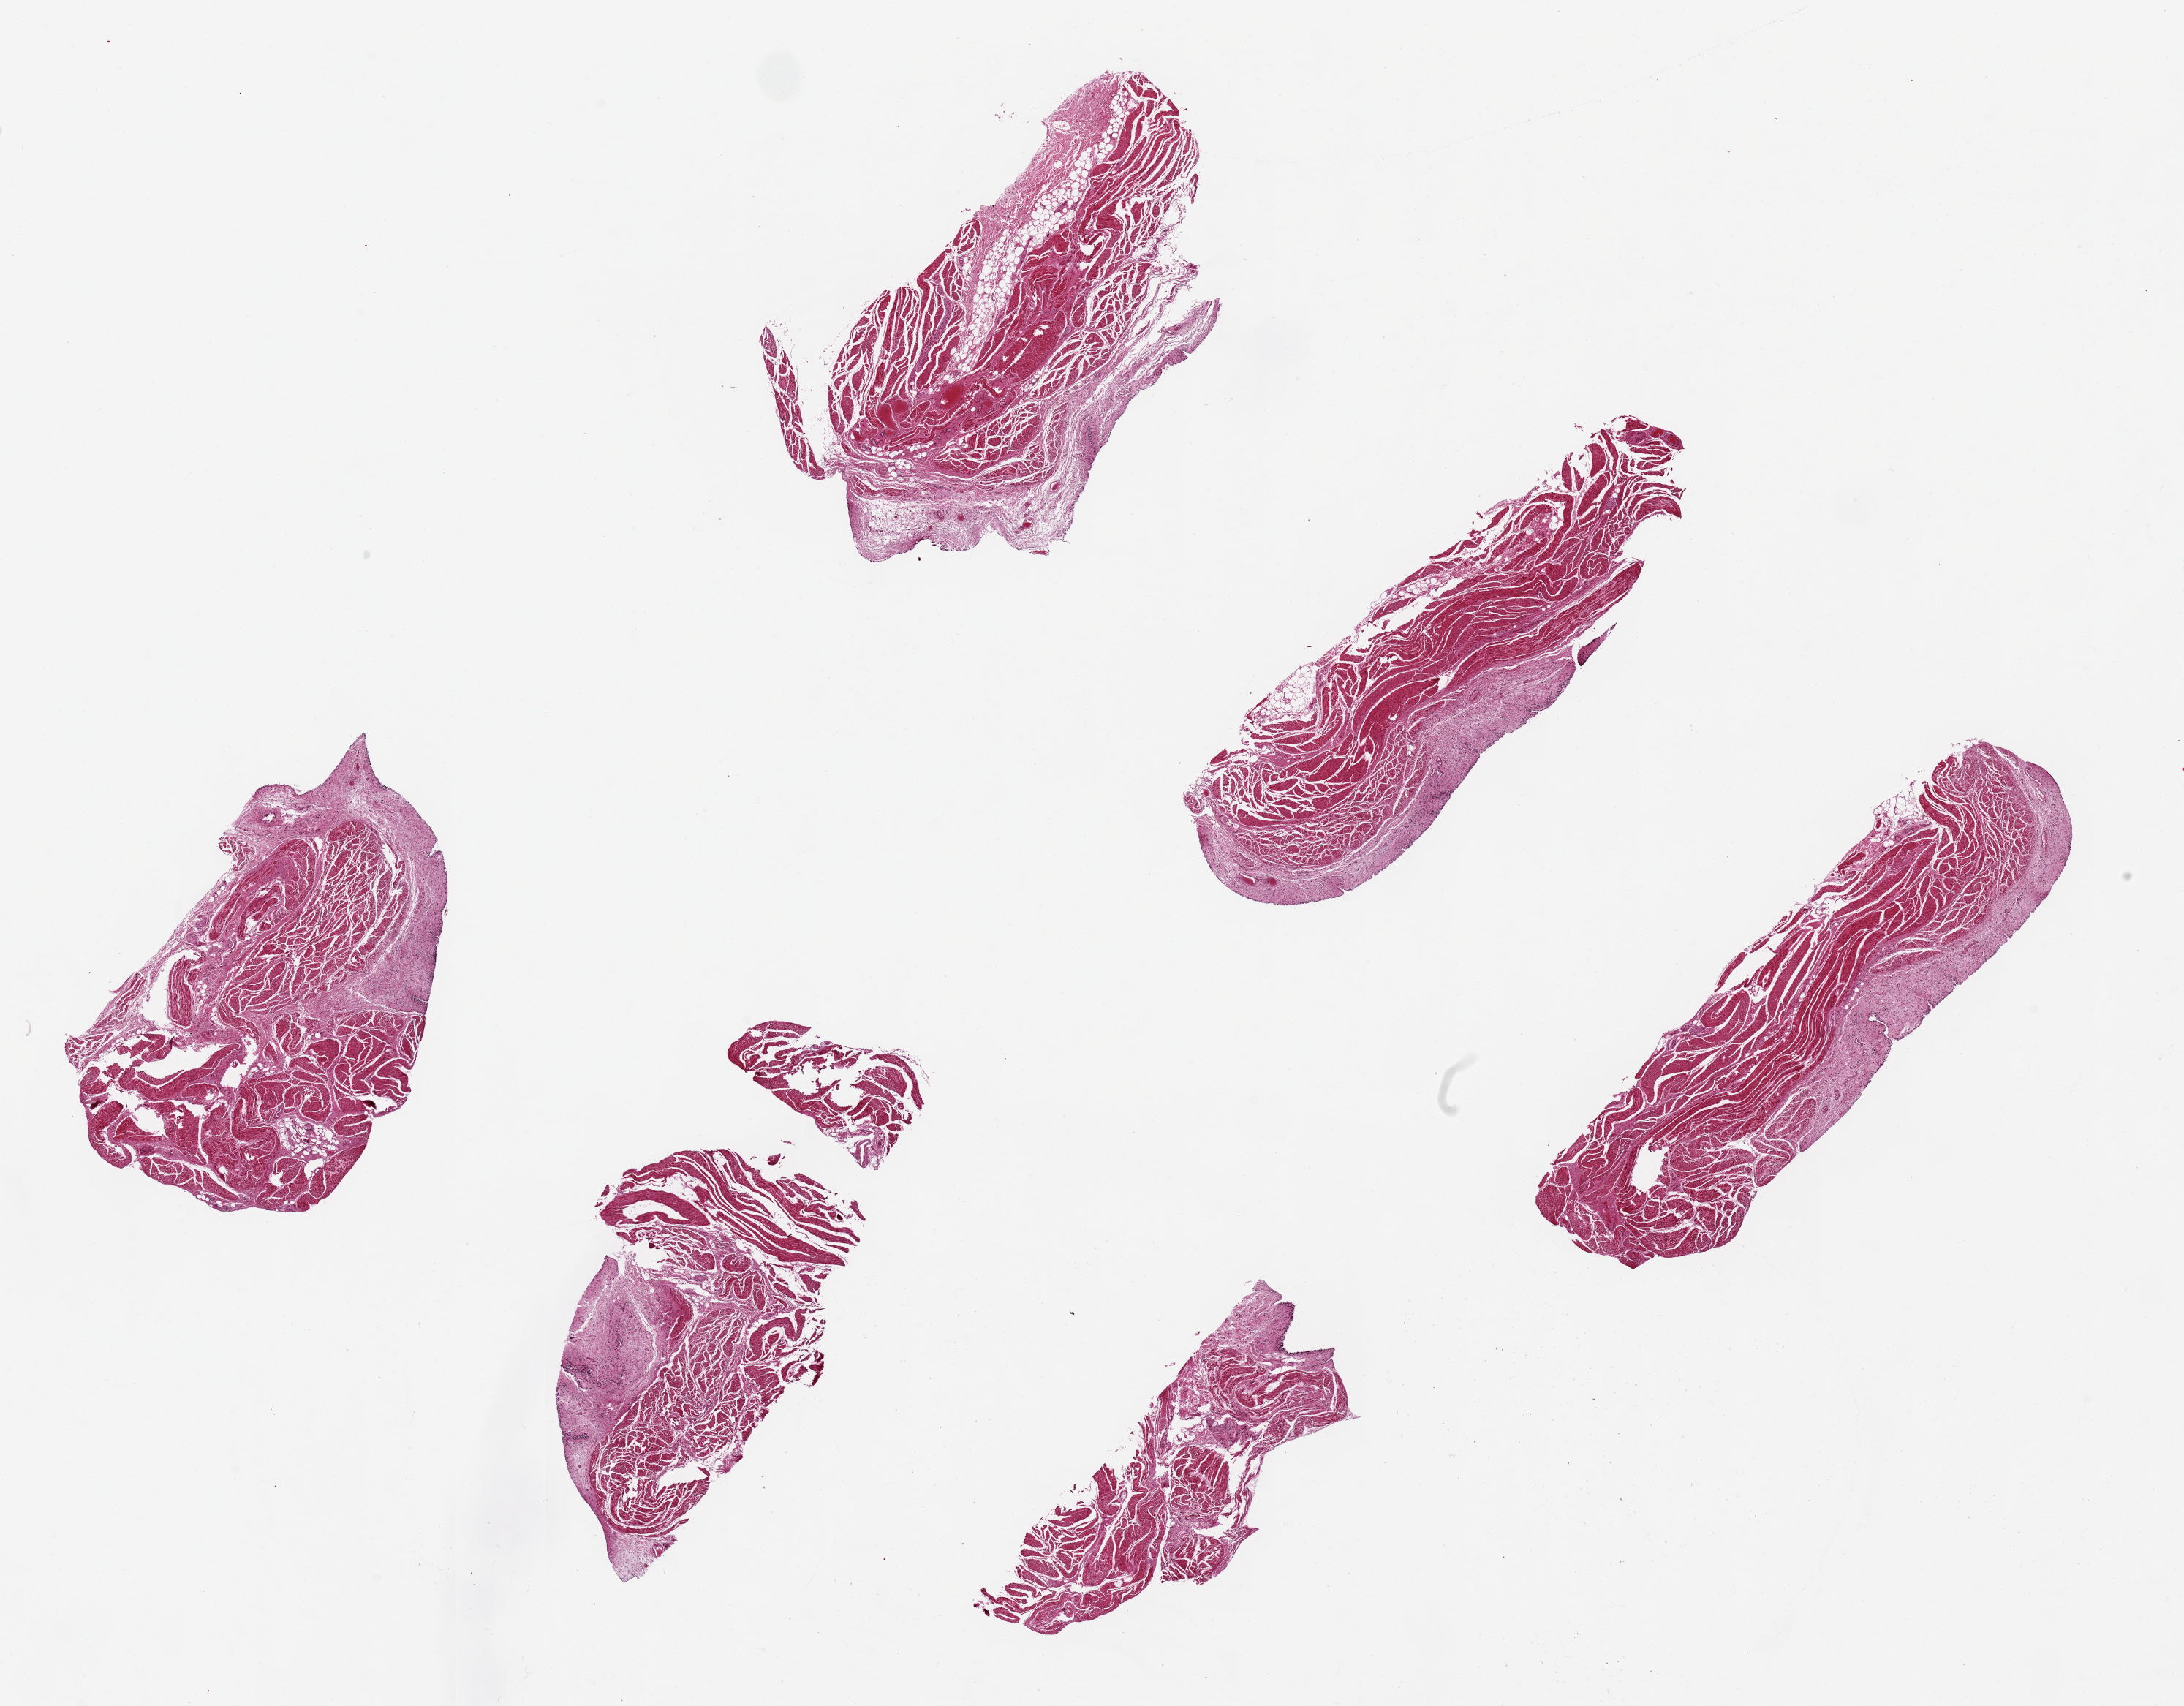
Hematoxylin and eosin (H&E) whole-slide image, shown as a low-resolution overview of the whole scanned area (about 23.6 x 18.5 mm). PAXgene-fixed, paraffin-embedded tissue. Target tissue: urinary bladder. Donor tissue sample. Donor: female.
Review note (as recorded): 6 pieces ~6x2.5mm, urothelium largely sloughed.